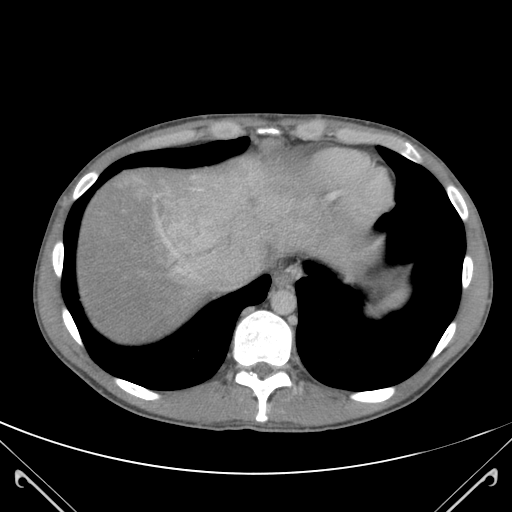
Contrast-enhanced abdominal CT (liver protocol), one axial slice. Slice 103 of 118 in the series (ordered by position). Soft-tissue window (W 400 / L 40 HU). 3 mm slice thickness. 512 × 512 image matrix, field of view 380 × 380 mm. From the clinical record (not read from this slice): diagnosis: hepatocellular carcinoma (patient treated with transarterial chemoembolisation; whether this scan precedes or follows treatment is not stated here); TNM stage (as recorded): Stage-IIIB; Child-Pugh class: A; tumour nodularity: uninodular.
Structures marked on this image (semi-automatic segmentation, software-assisted and operator-edited):
- abdominal aorta: bounding box <273,289,295,313> (left, top, right, bottom; pixels)
- liver parenchyma outside the tumour (the mass and vessels are separate outlines, so this box may not span the whole liver): <76,155,307,345>
- mass: <151,173,266,261>
- liver vessels: <155,172,257,280>